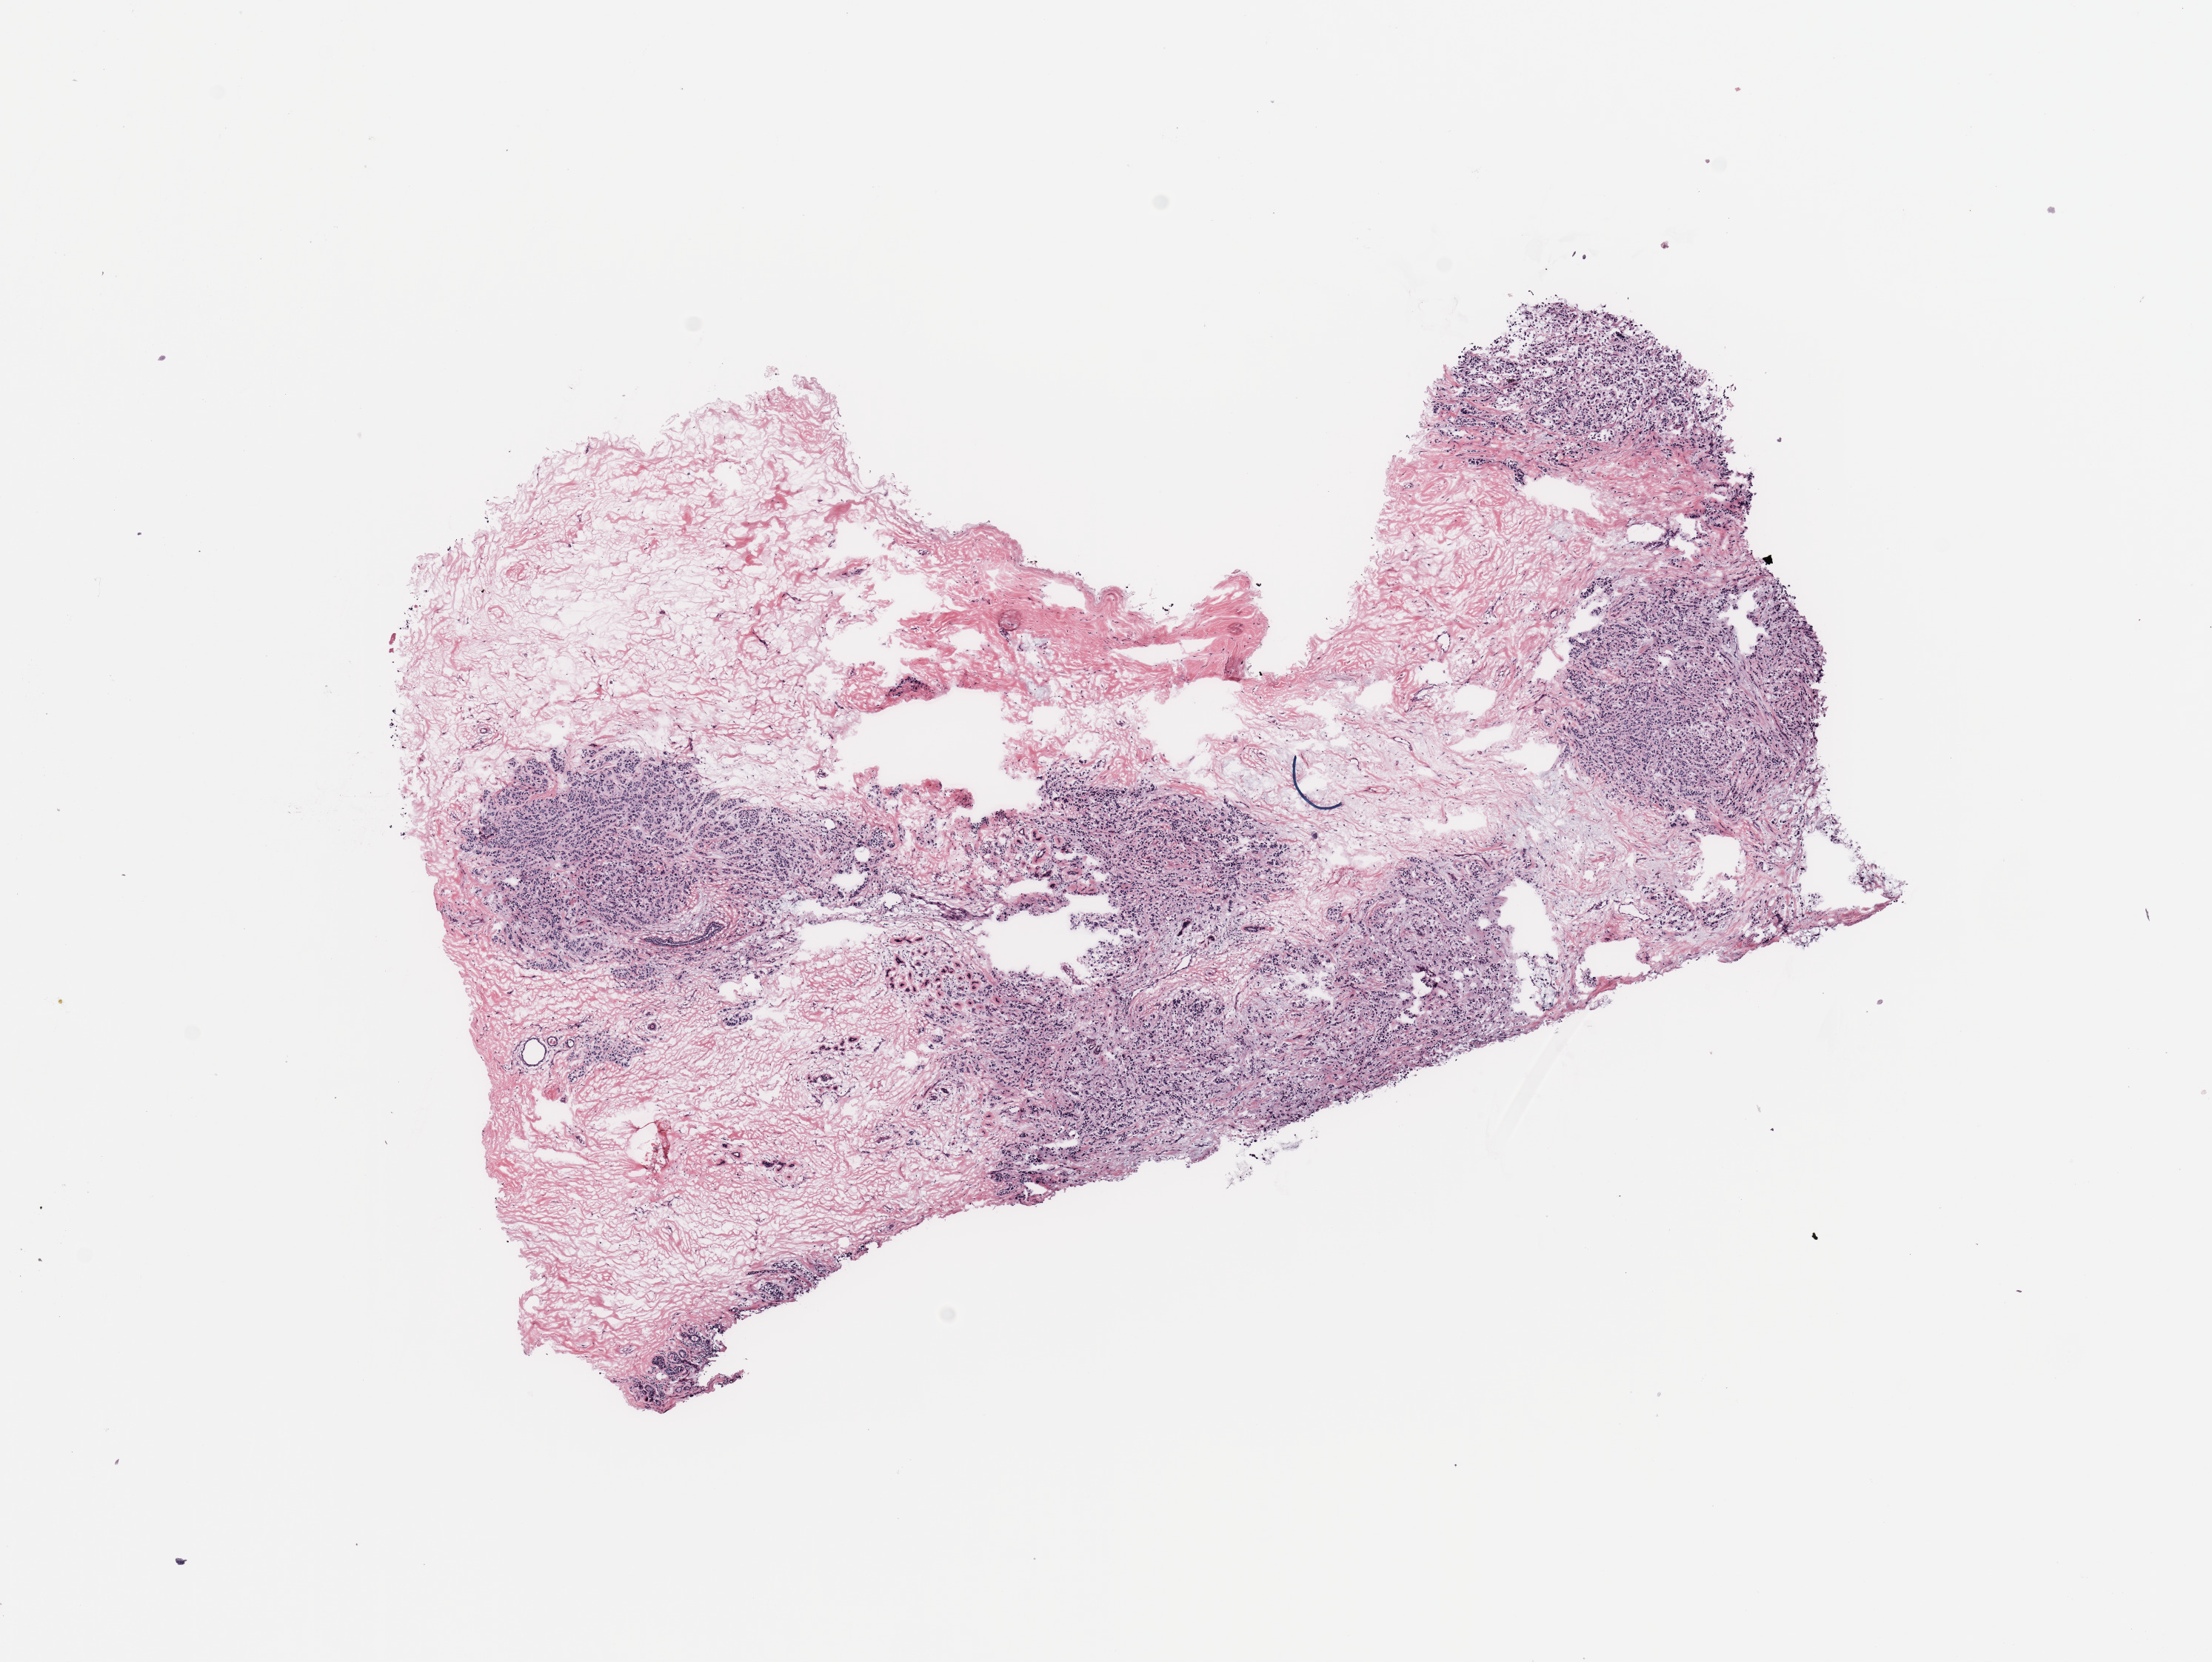
Digitized H&E-stained tissue section (whole slide), low-resolution overview of the scanned area, about 11.8 x 8.9 mm, tumour tissue sample, breast. Patient: female, age 71 years.
AJCC pathologic stage: IIIA. Diagnosis: Invasive lobular carcinoma.